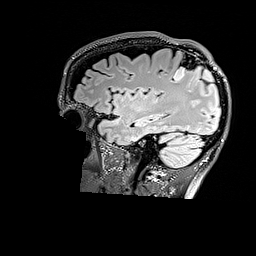
Brain MRI from a brain-tumour surgery series, one sagittal slice; position 123 of 176 along the scan axis; T2 FLAIR; 1 mm slice thickness; 256 × 256 image matrix, field of view 256 × 256 mm. Case-level facts recorded for this patient, not image findings: histopathology: Astrocytoma; WHO grade: 3; IDH mutation: yes; tumour location: Right Parietal.
Outlined on this slice (outlined manually by an expert reader):
- tumour: box from (x=174, y=64) to (x=210, y=80) px